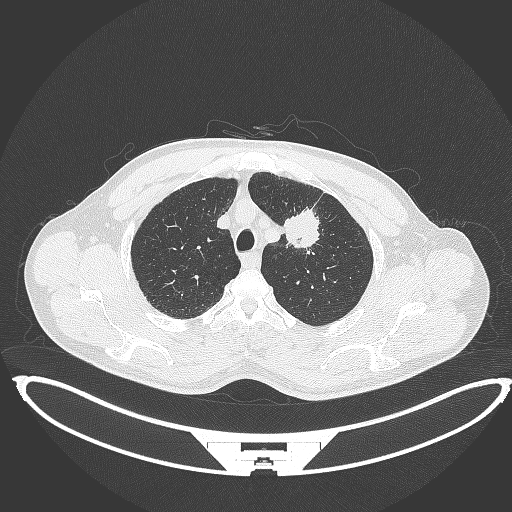
Chest CT, one axial slice. Position 358 of 395 along the scan axis. Lung window (W 1500 / L -600 HU). 1 mm slice thickness. 512 × 512 image matrix. Male patient, age 60 years. Case-level facts recorded for this patient, not image findings: clinical TNM (as recorded): T2a N0 M0; histopathological grade: G1-G2.
Structures marked on this image (bounding box drawn by a radiologist):
- lung tumour (recorded histology: squamous cell carcinoma): bounding box <281,207,325,253> (left, top, right, bottom; pixels)